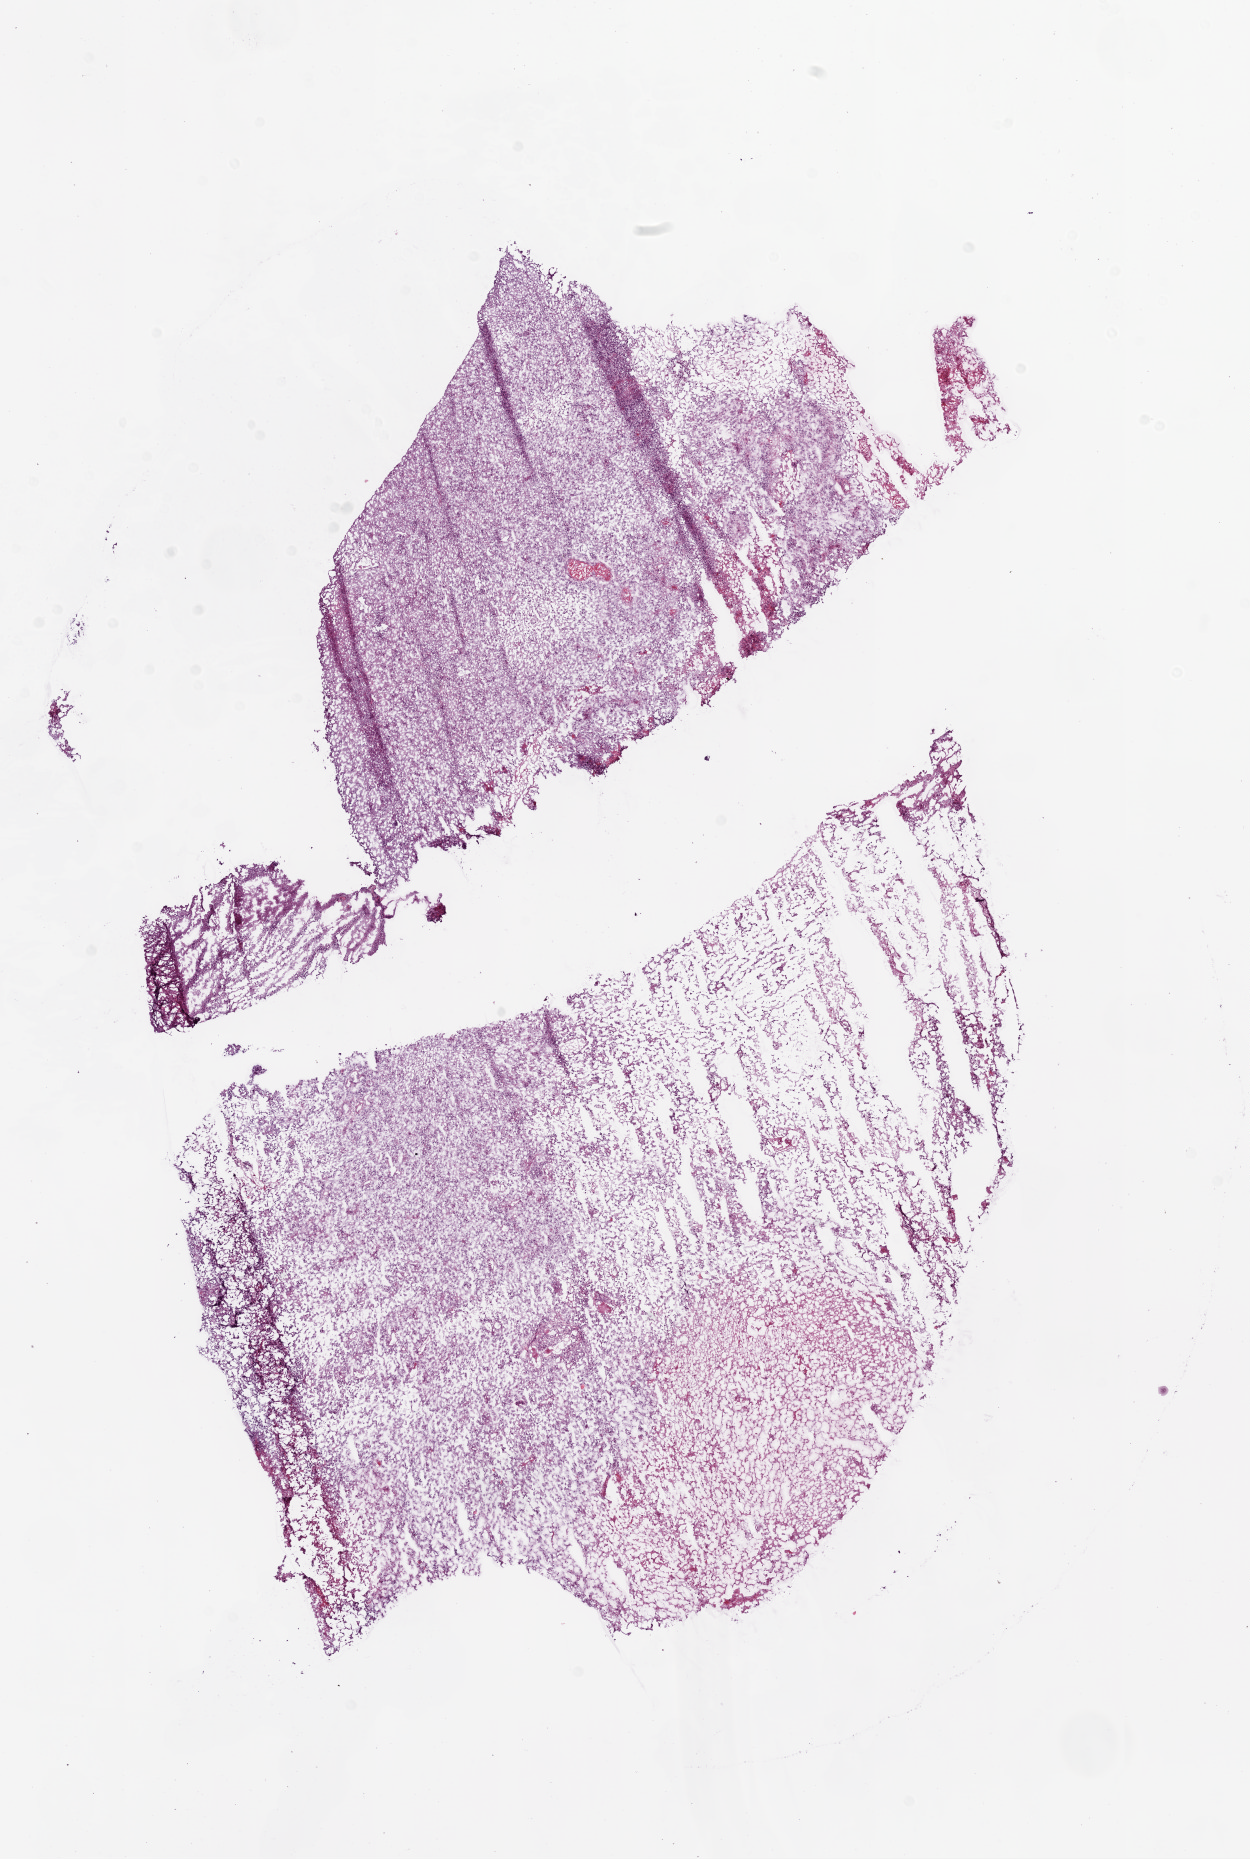
H&E-stained whole-slide image — whole scanned area (about 10.0 x 14.9 mm, slide scanned at 20x) shown as a low-resolution overview. Frozen section from the bottom of the tissue portion. Sample: primary tumour, brain. Male, age 48 years at initial diagnosis. Composition of this section per pathologist review: tumour cells 75%, tumour nuclei 85%, normal cells 0%, stromal cells 5%, necrosis 20%.
Diagnosis: Glioblastoma.